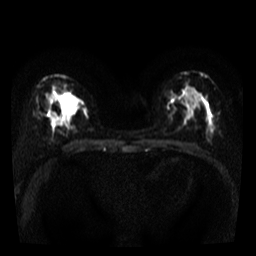
Breast MRI, one axial slice. Slice 20 of 40 in the series (ordered by position). Diffusion-weighted series; image 2 of 4 stored at this slice position (different b-values; order by instance number). 3 T. 256 × 256 image matrix, field of view 280 × 280 mm. Female patient.
Annotated regions visible in this slice (outlined manually by an expert reader):
- tumour on diffusion-weighted imaging: box from (x=67, y=97) to (x=80, y=113) px